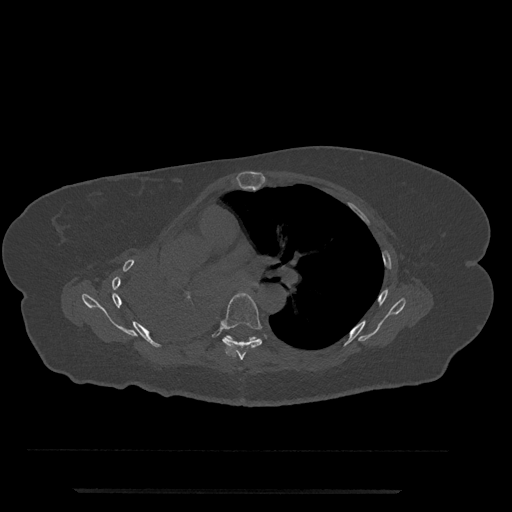
CT including the spine, one axial slice. Position 487 of 797 along the scan axis. Reconstruction kernel Br40s/3. Bone window (W 1800 / L 400 HU). 512 × 512 image matrix, field of view 440 × 440 mm. Patient: female, 51 years. From the clinical record (not read from this slice): primary cancer: neuro.
Annotated regions visible in this slice (semi-automatically segmented with operator editing):
- T6 vertebra: bounding box <221,292,262,360> (left, top, right, bottom; pixels)
- T7 vertebra: <227,335,257,341>